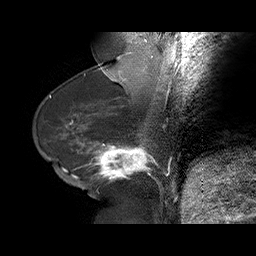
Breast MRI (dynamic contrast-enhanced), one sagittal slice. Position 28 of 75 along the scan axis. Dynamic contrast-enhanced series, time point 2 of 6 at this slice position (early post-contrast). 1.5 T. TE 4.5 ms, TR 32.4 ms. 256 × 256 image matrix, field of view 180 × 180 mm. Female patient. From the clinical record (not read from this slice): setting: breast cancer imaged before/during neoadjuvant chemotherapy; receptor status: HR-positive, HER2-negative.
Structures marked on this image (semi-automatic segmentation, software-assisted and operator-edited):
- analysis volume of interest (the breast-tissue region the enhancement analysis was run in; not a lesion): bounding box (x1, y1, x2, y2) in pixels: (58, 134, 166, 191)
- tumour enhancement mask (voxels above the 100 % enhancement threshold inside the analysis volume of interest): (62, 142, 152, 181)